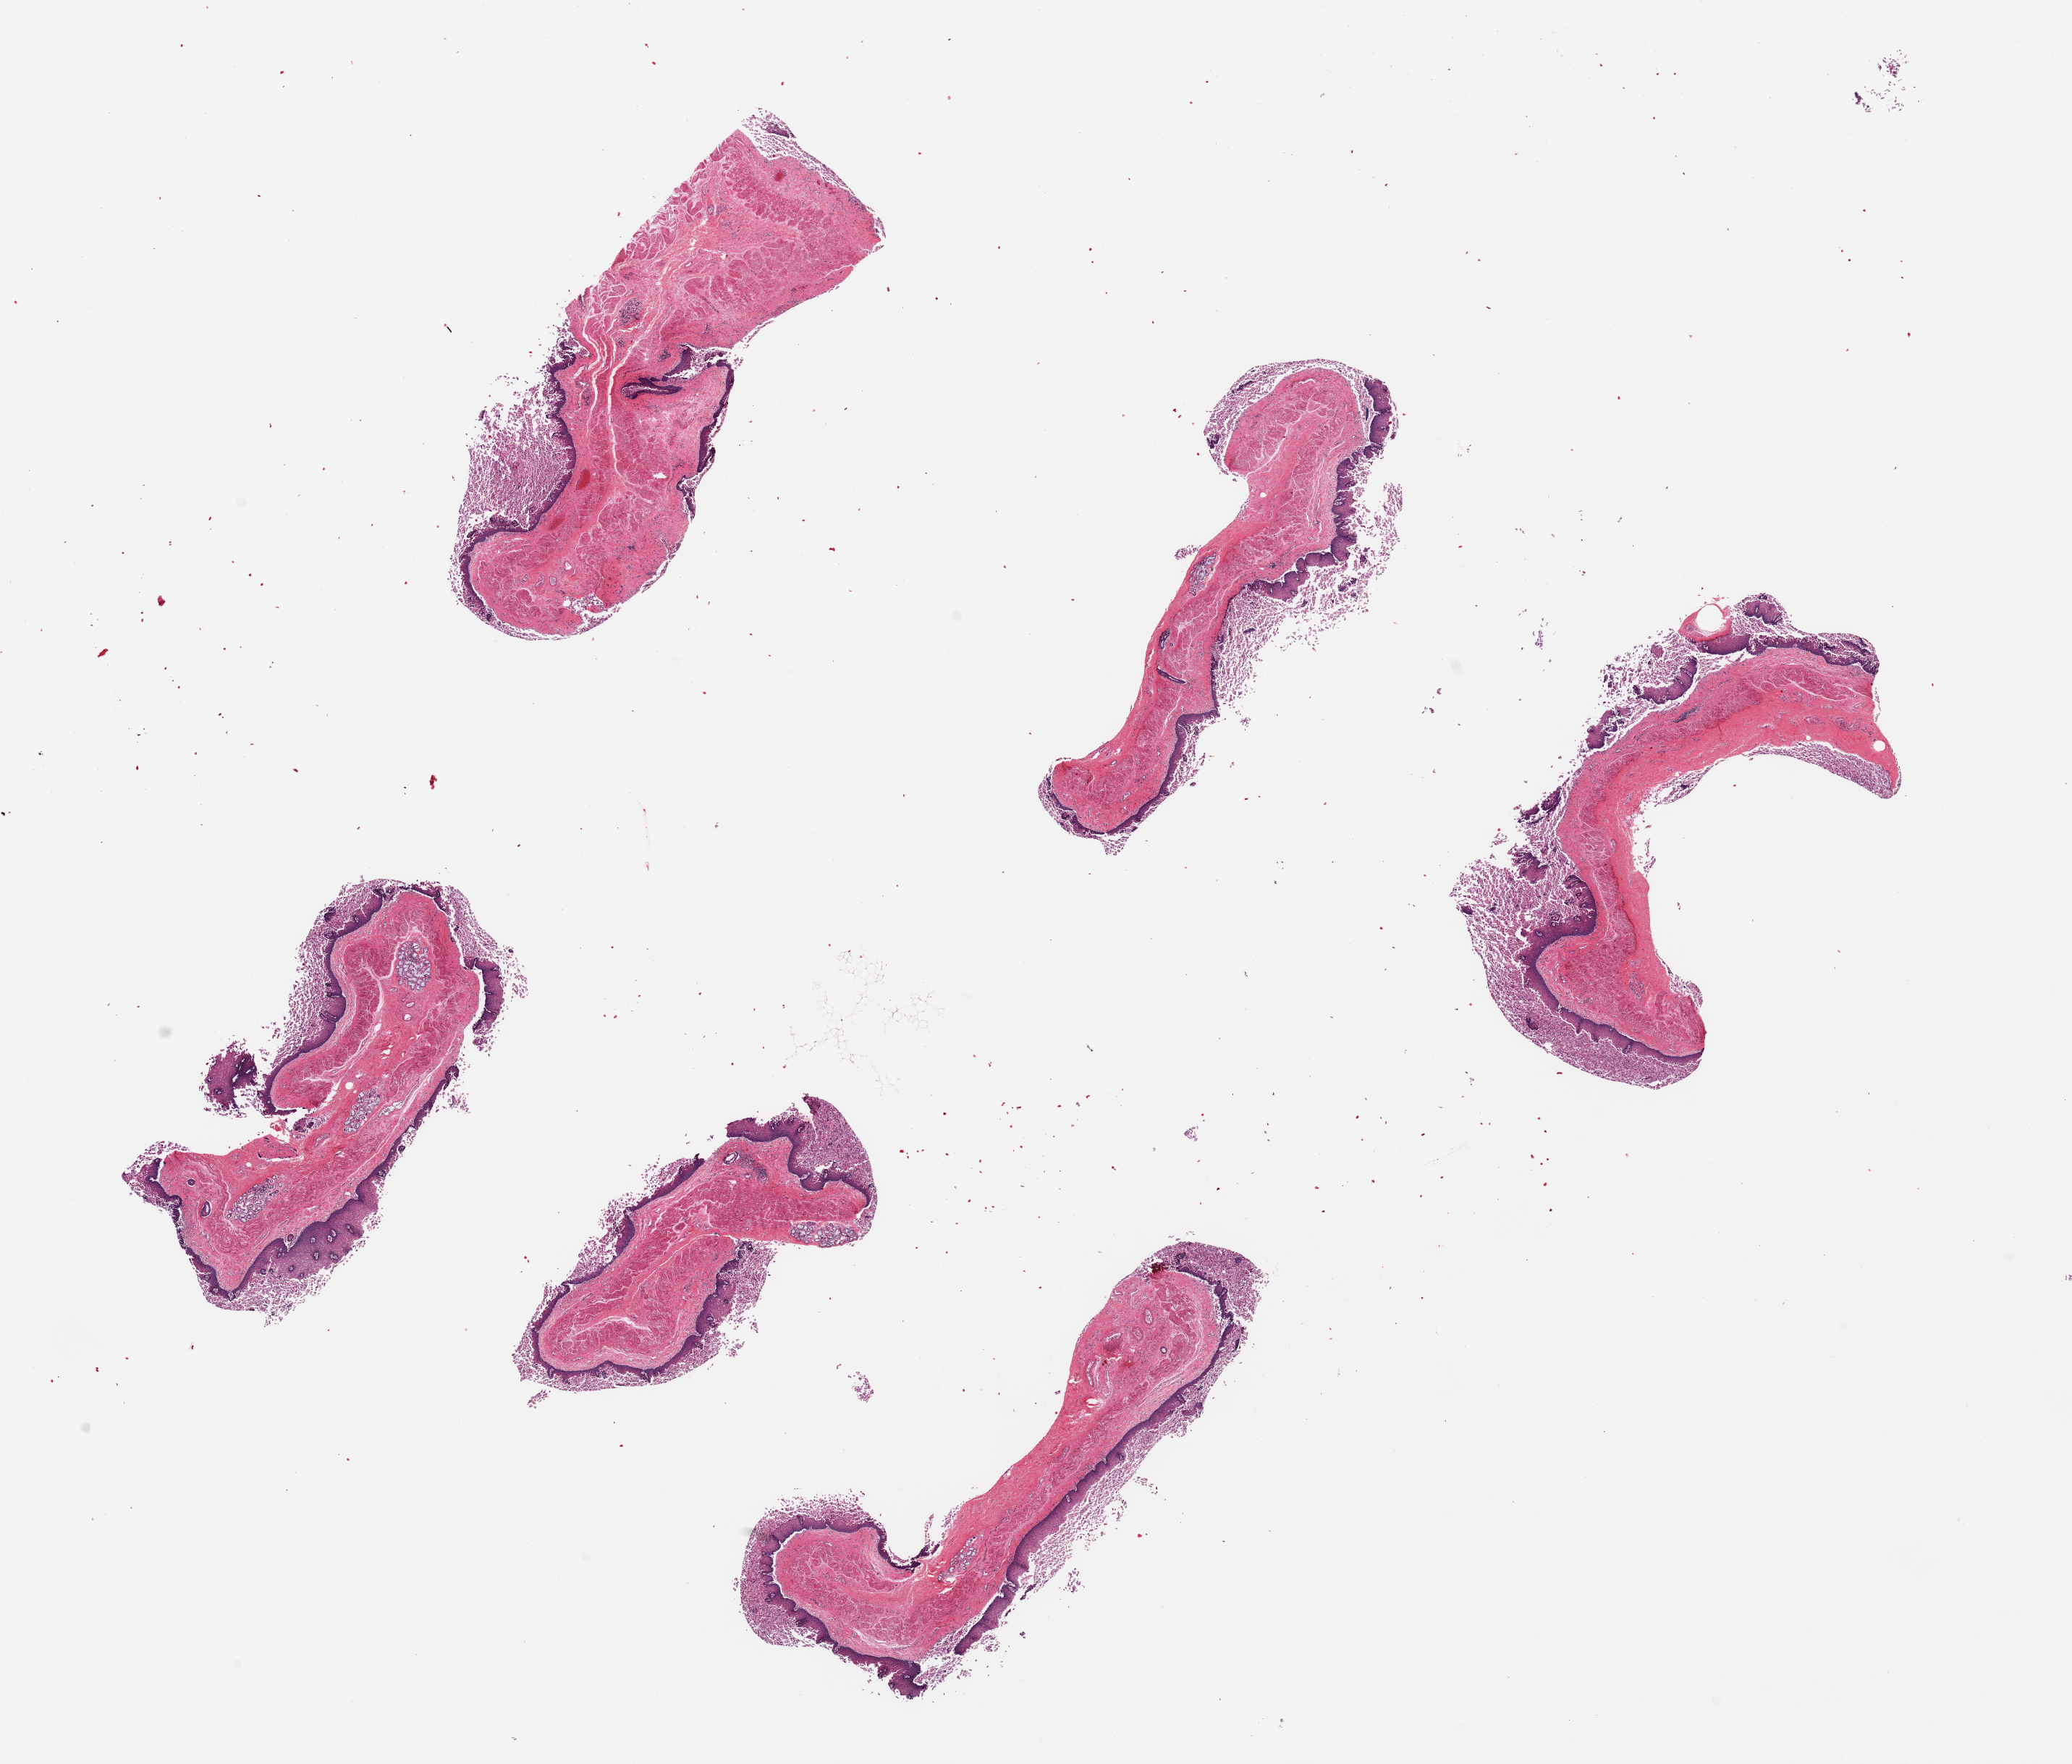
Whole-slide image, hematoxylin and eosin (H&E) stain — low-resolution overview of the scanned area, about 22.6 x 19.3 mm, PAXgene-fixed paraffin-embedded (PFPE) section, section of esophageal mucous membrane (target tissue), tissue donor sample. Donor: female.
Pathologist's review note for this sample: 6 pieces, up to 6x2mm; considerable surface sloughing.